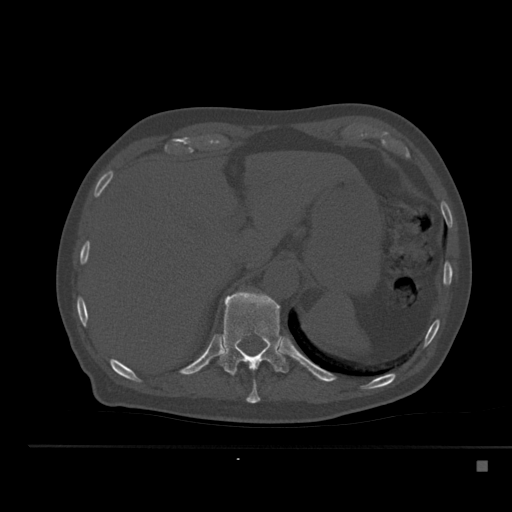
CT including the spine, one axial slice. Position 251 of 517 along the scan axis. Reconstruction kernel Br40s. Bone window (W 1800 / L 400 HU). 1.5 mm slice thickness. 512 × 512 image matrix. Male patient, age 70 years. Case-level facts recorded for this patient, not image findings: primary cancer: renal.
Annotated regions visible in this slice (semi-automatically segmented with operator editing):
- T10 vertebra: bounding box (x1, y1, x2, y2) in pixels: (246, 380, 260, 403)
- T11 vertebra: (218, 290, 288, 376)